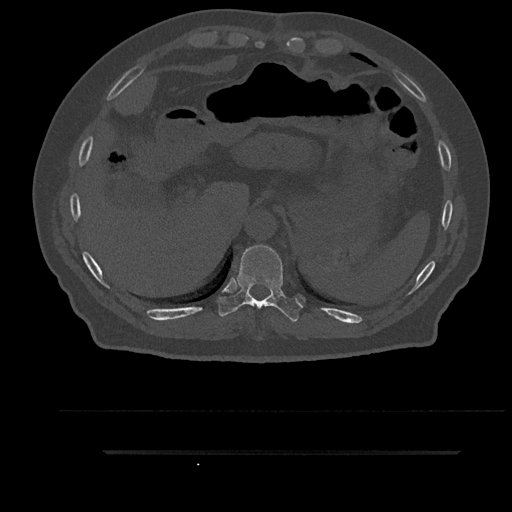
CT including the spine, one axial slice. Bone window (W 1800 / L 400 HU). 512 × 512 image matrix. Patient: male, 63 years. Case-level facts recorded for this patient, not image findings: primary cancer: renal; vertebrae with lytic lesions (as recorded): T8.
Annotated regions visible in this slice (semi-automatically segmented with operator editing):
- T10 vertebra: bounding box (x1, y1, x2, y2) in pixels: (218, 245, 303, 322)